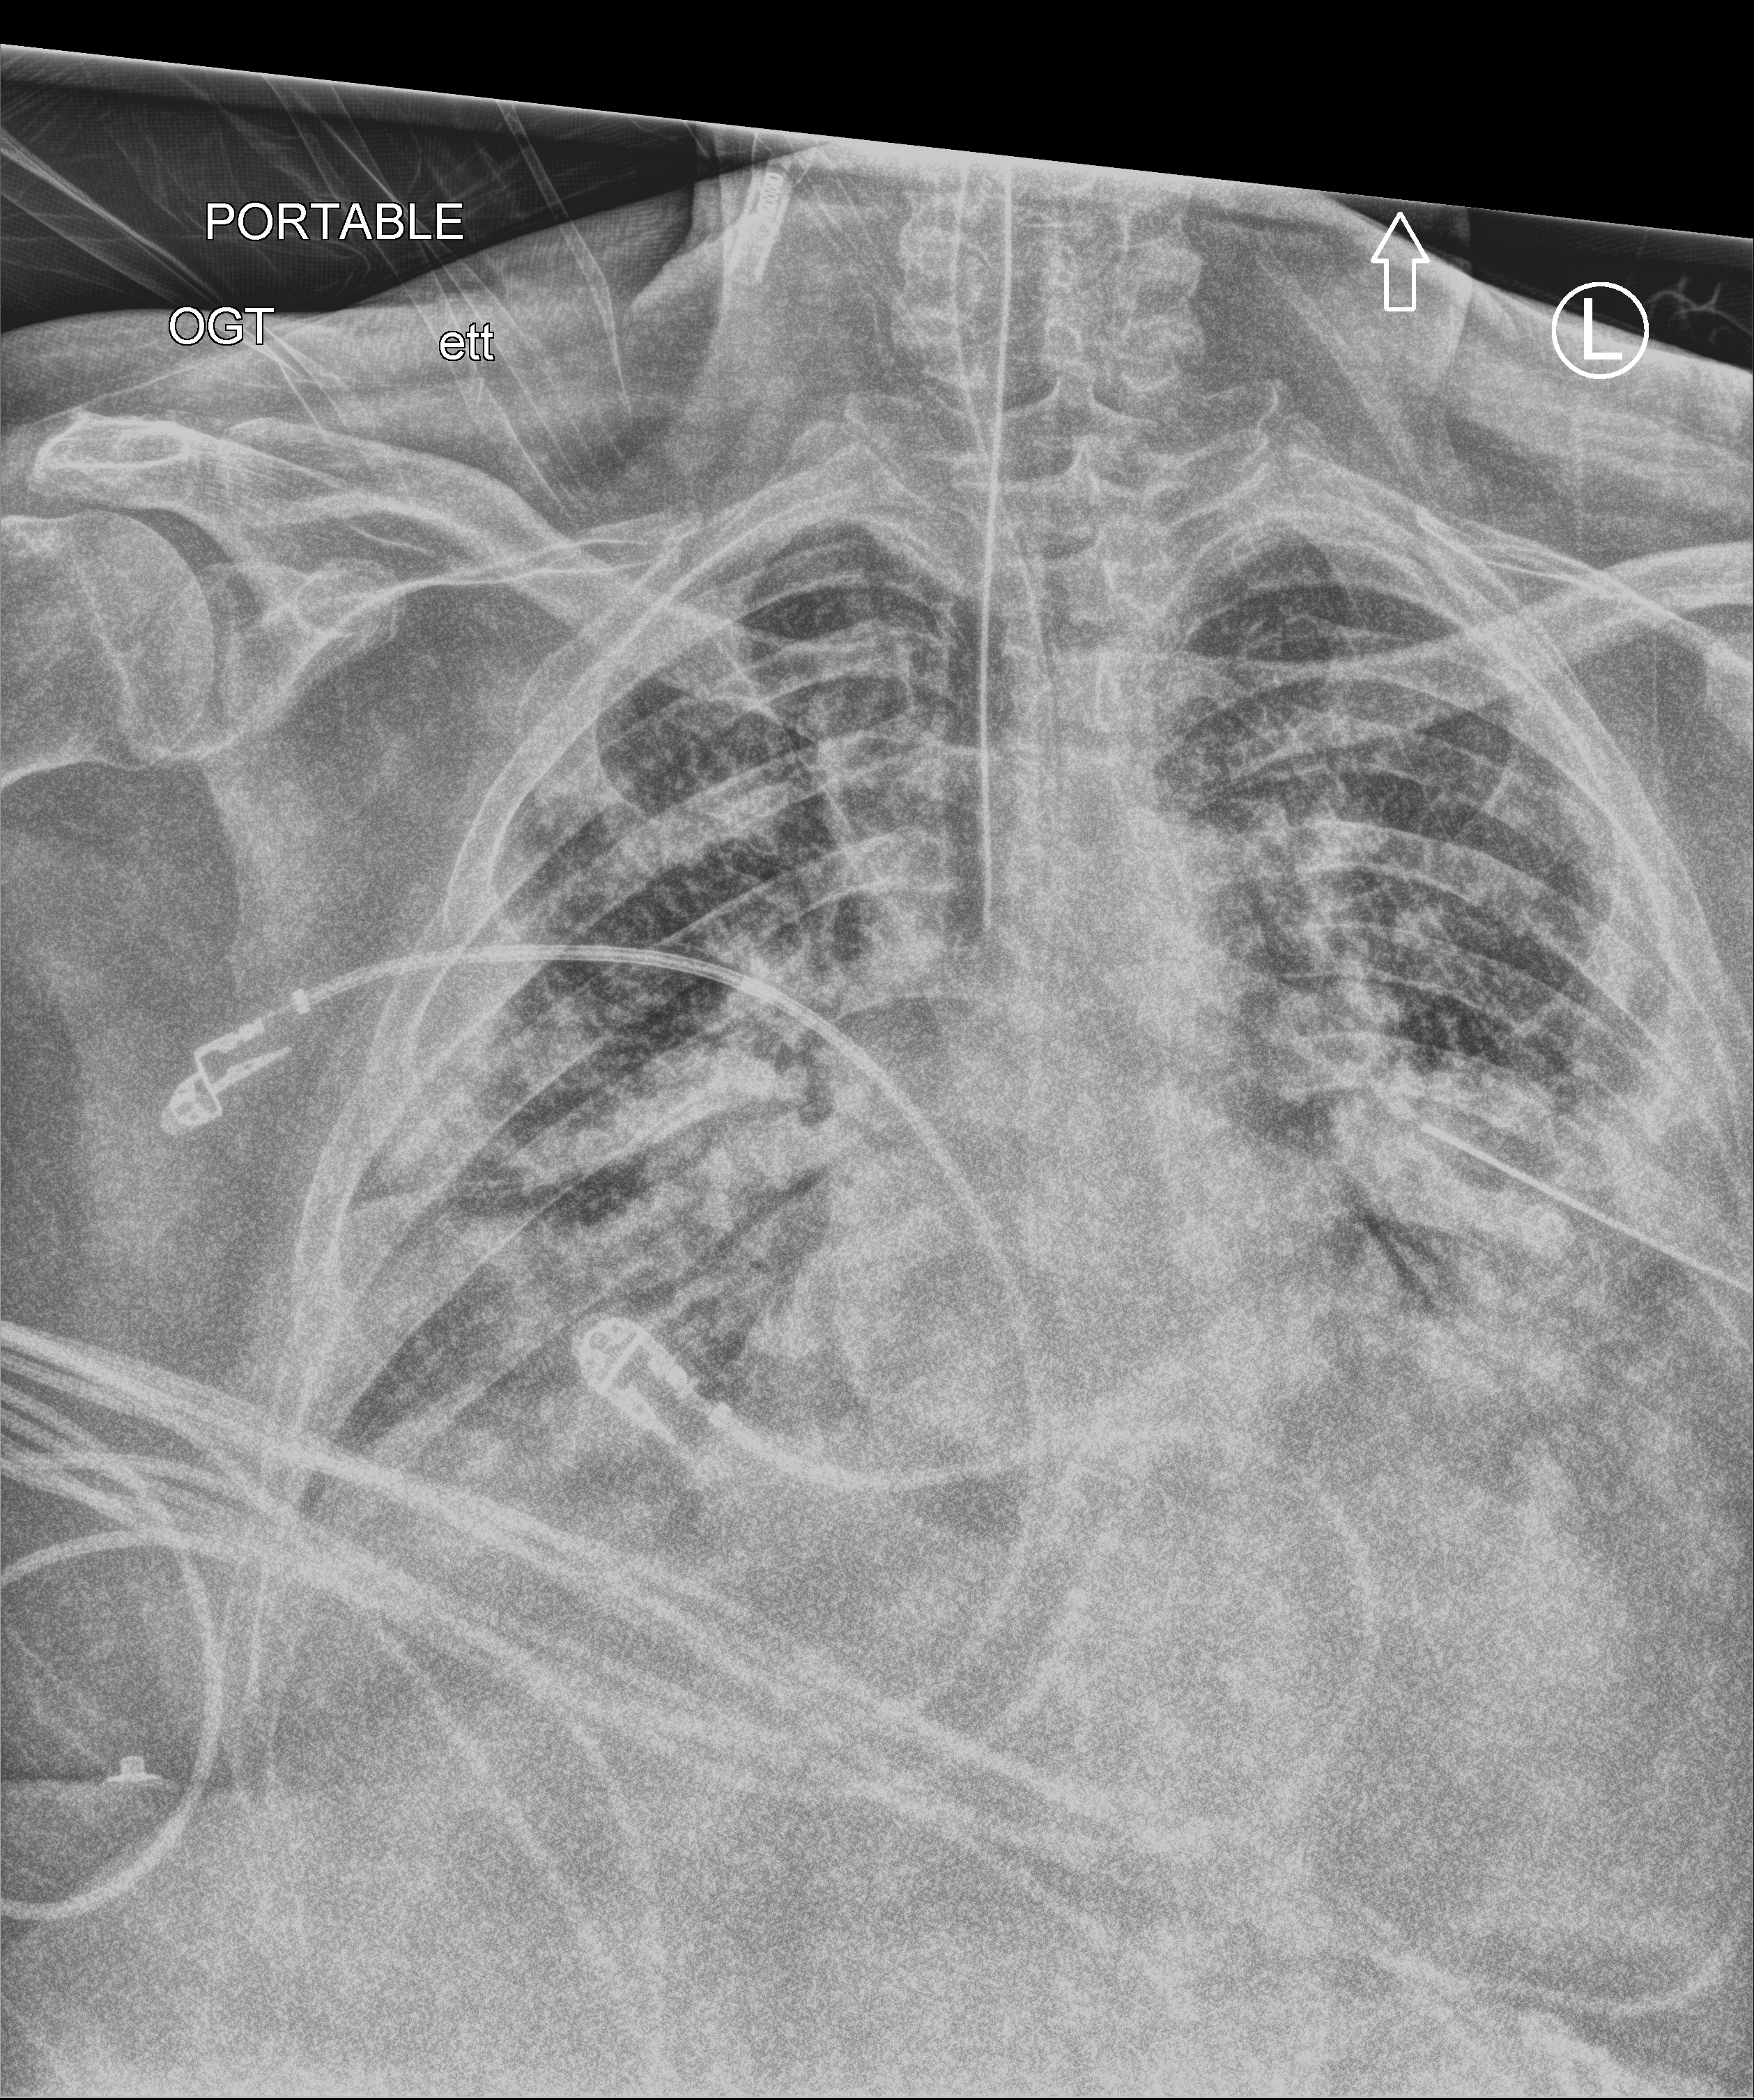
Chest X-ray (portable), anteroposterior (AP) projection. Patient hospitalised with COVID-19; male, aged 60–74 years.
Hospital-stay facts (about this admission, not read from this image; timing relative to this image not recorded):
- admitted to intensive care during this hospital stay: yes